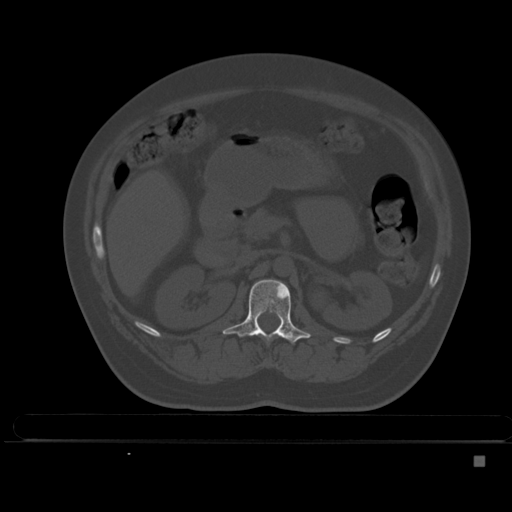
CT including the spine, one axial slice; slice 196 of 495 in the series (ordered by position); bone window (W 1800 / L 400 HU); 1.5 mm slice thickness; 512 × 512 image matrix. Patient: female, 33 years. Case-level facts recorded for this patient, not image findings: primary cancer: breast; vertebrae with lytic lesions (as recorded): T1.
Structures marked on this image (semi-automatic segmentation, software-assisted and operator-edited):
- L1 vertebra: bounding box (x1, y1, x2, y2) in pixels: (222, 279, 311, 344)